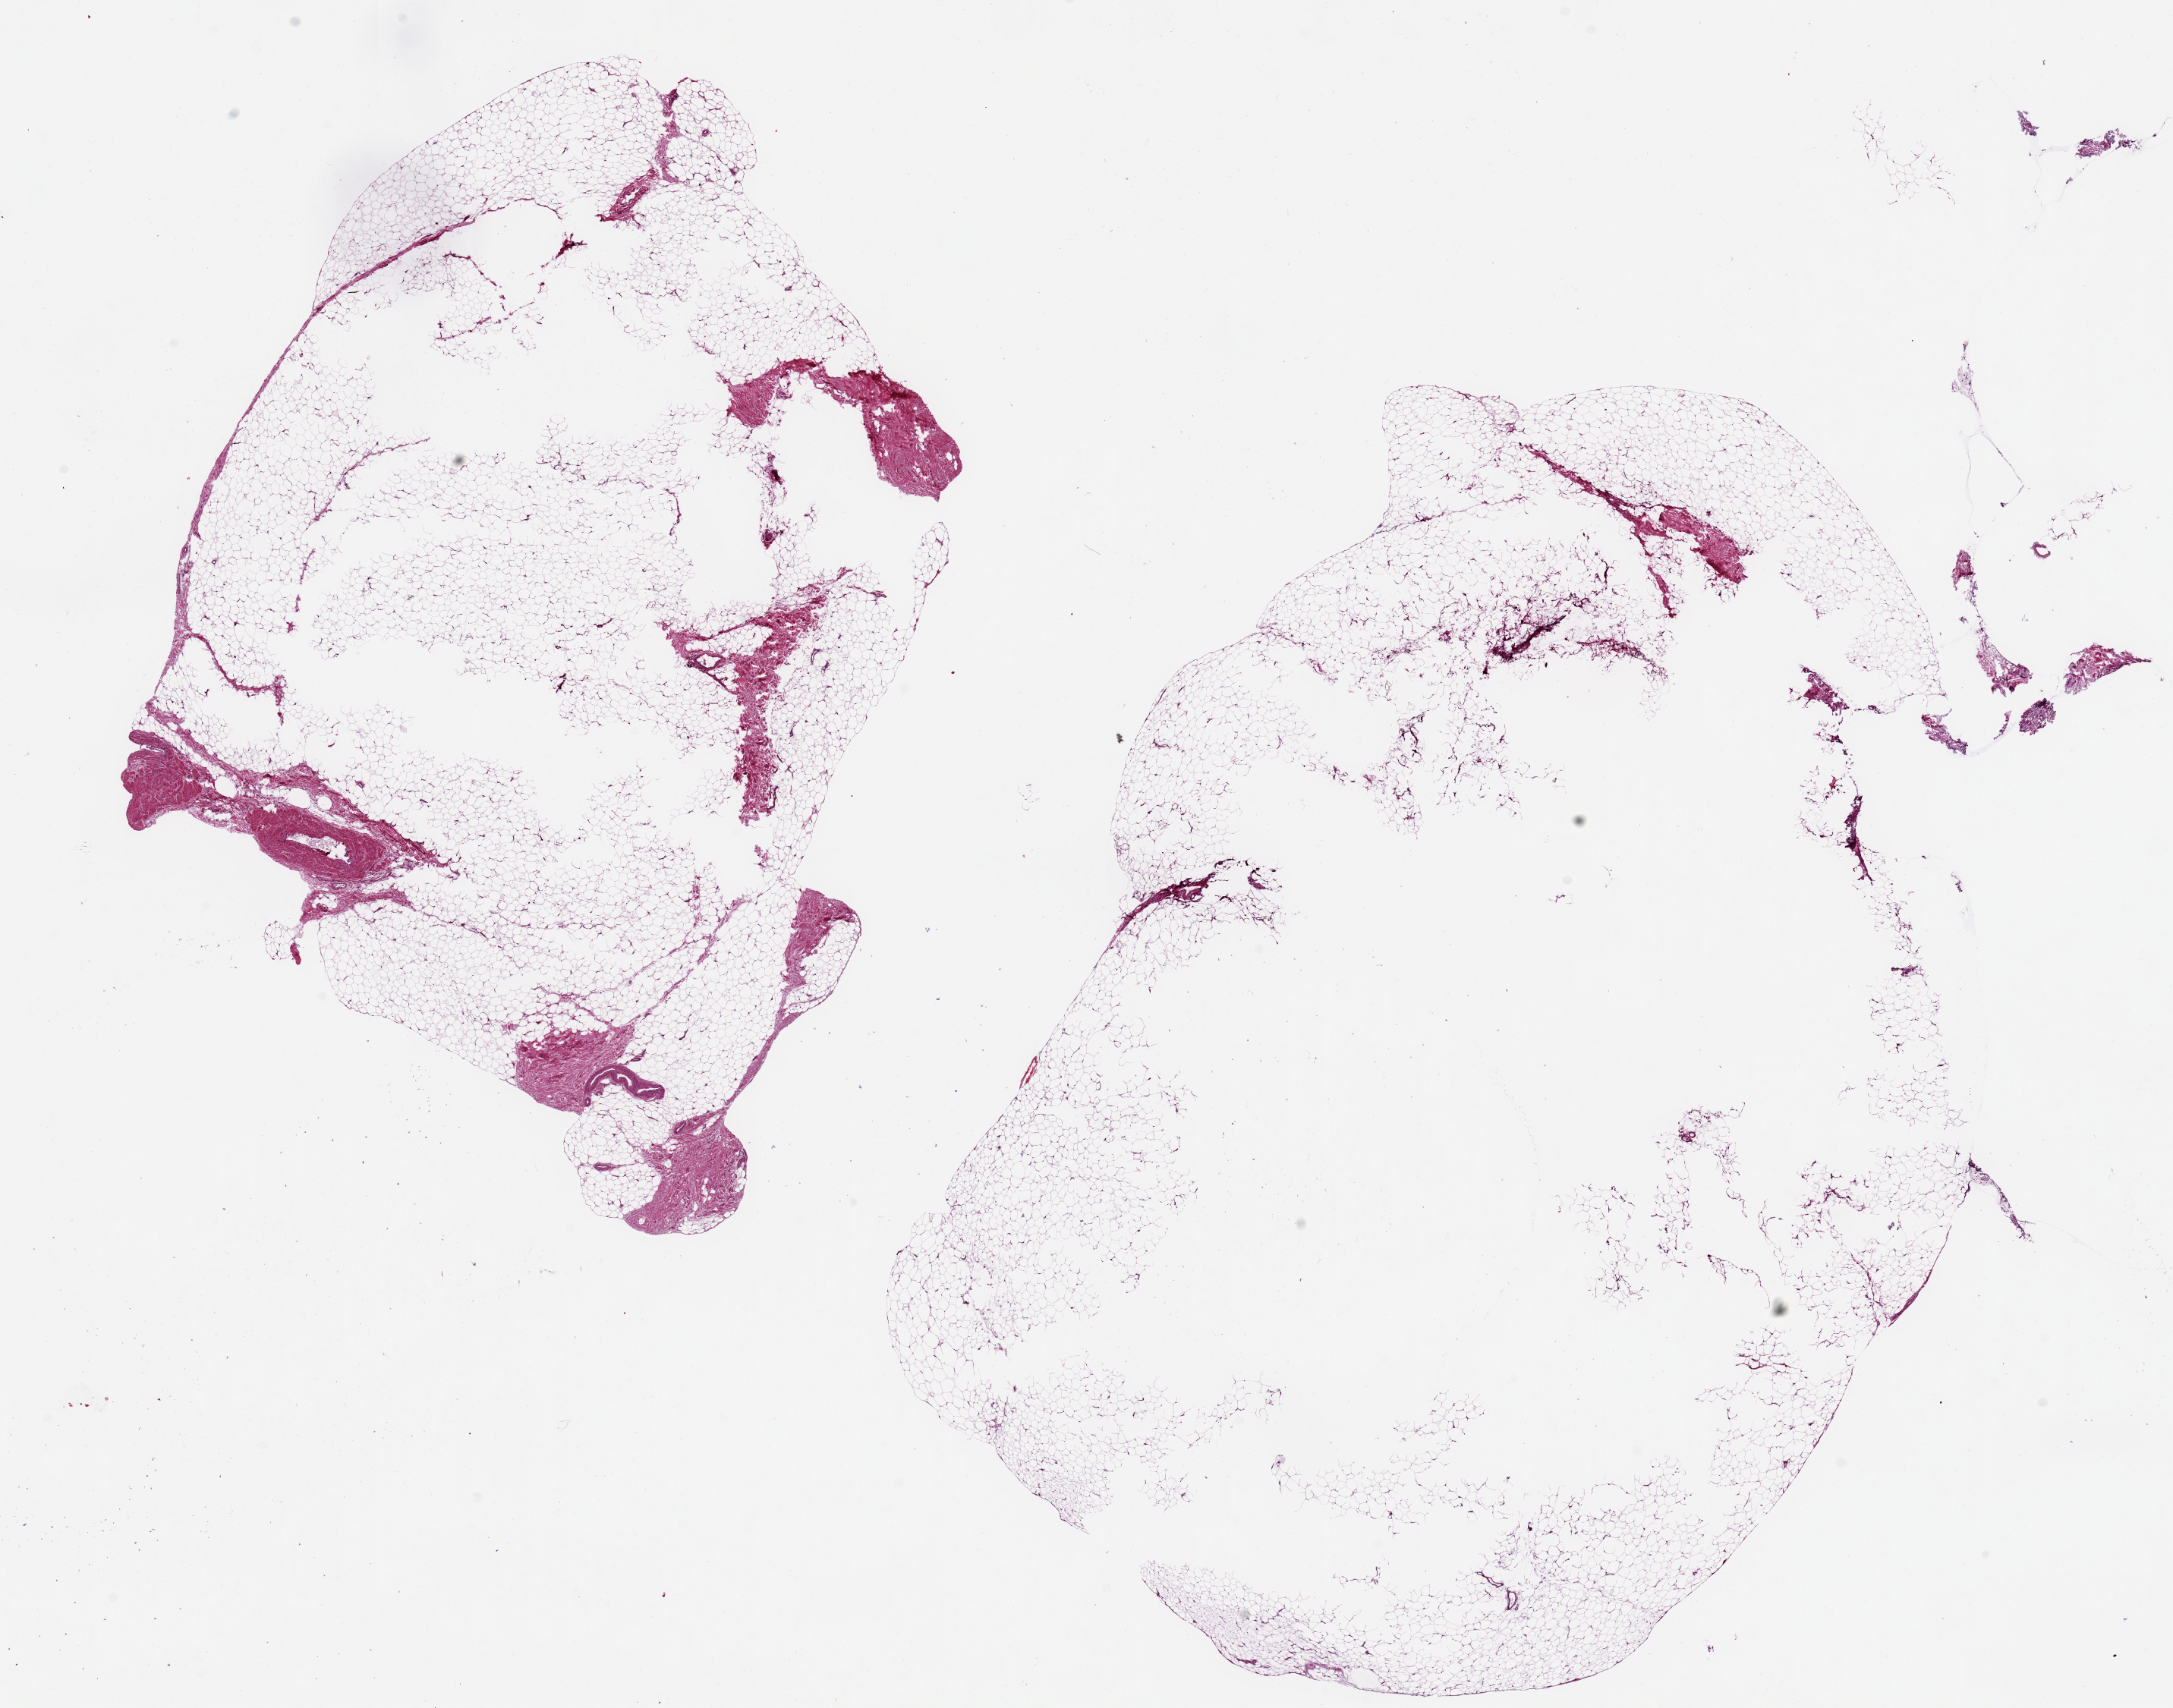
Hematoxylin and eosin (H&E) whole-slide image, brightfield, shown as a low-resolution overview of the whole scanned area (about 22.6 x 17.8 mm, acquisition: 20x scan). PAXgene-fixed paraffin-embedded (PFPE) section. Section of adipose tissue (target tissue). Donor tissue sample.
Reviewer comment on this tissue sample: 2 pieces 10x8 & 13x10 with large central hollow fixation defects.